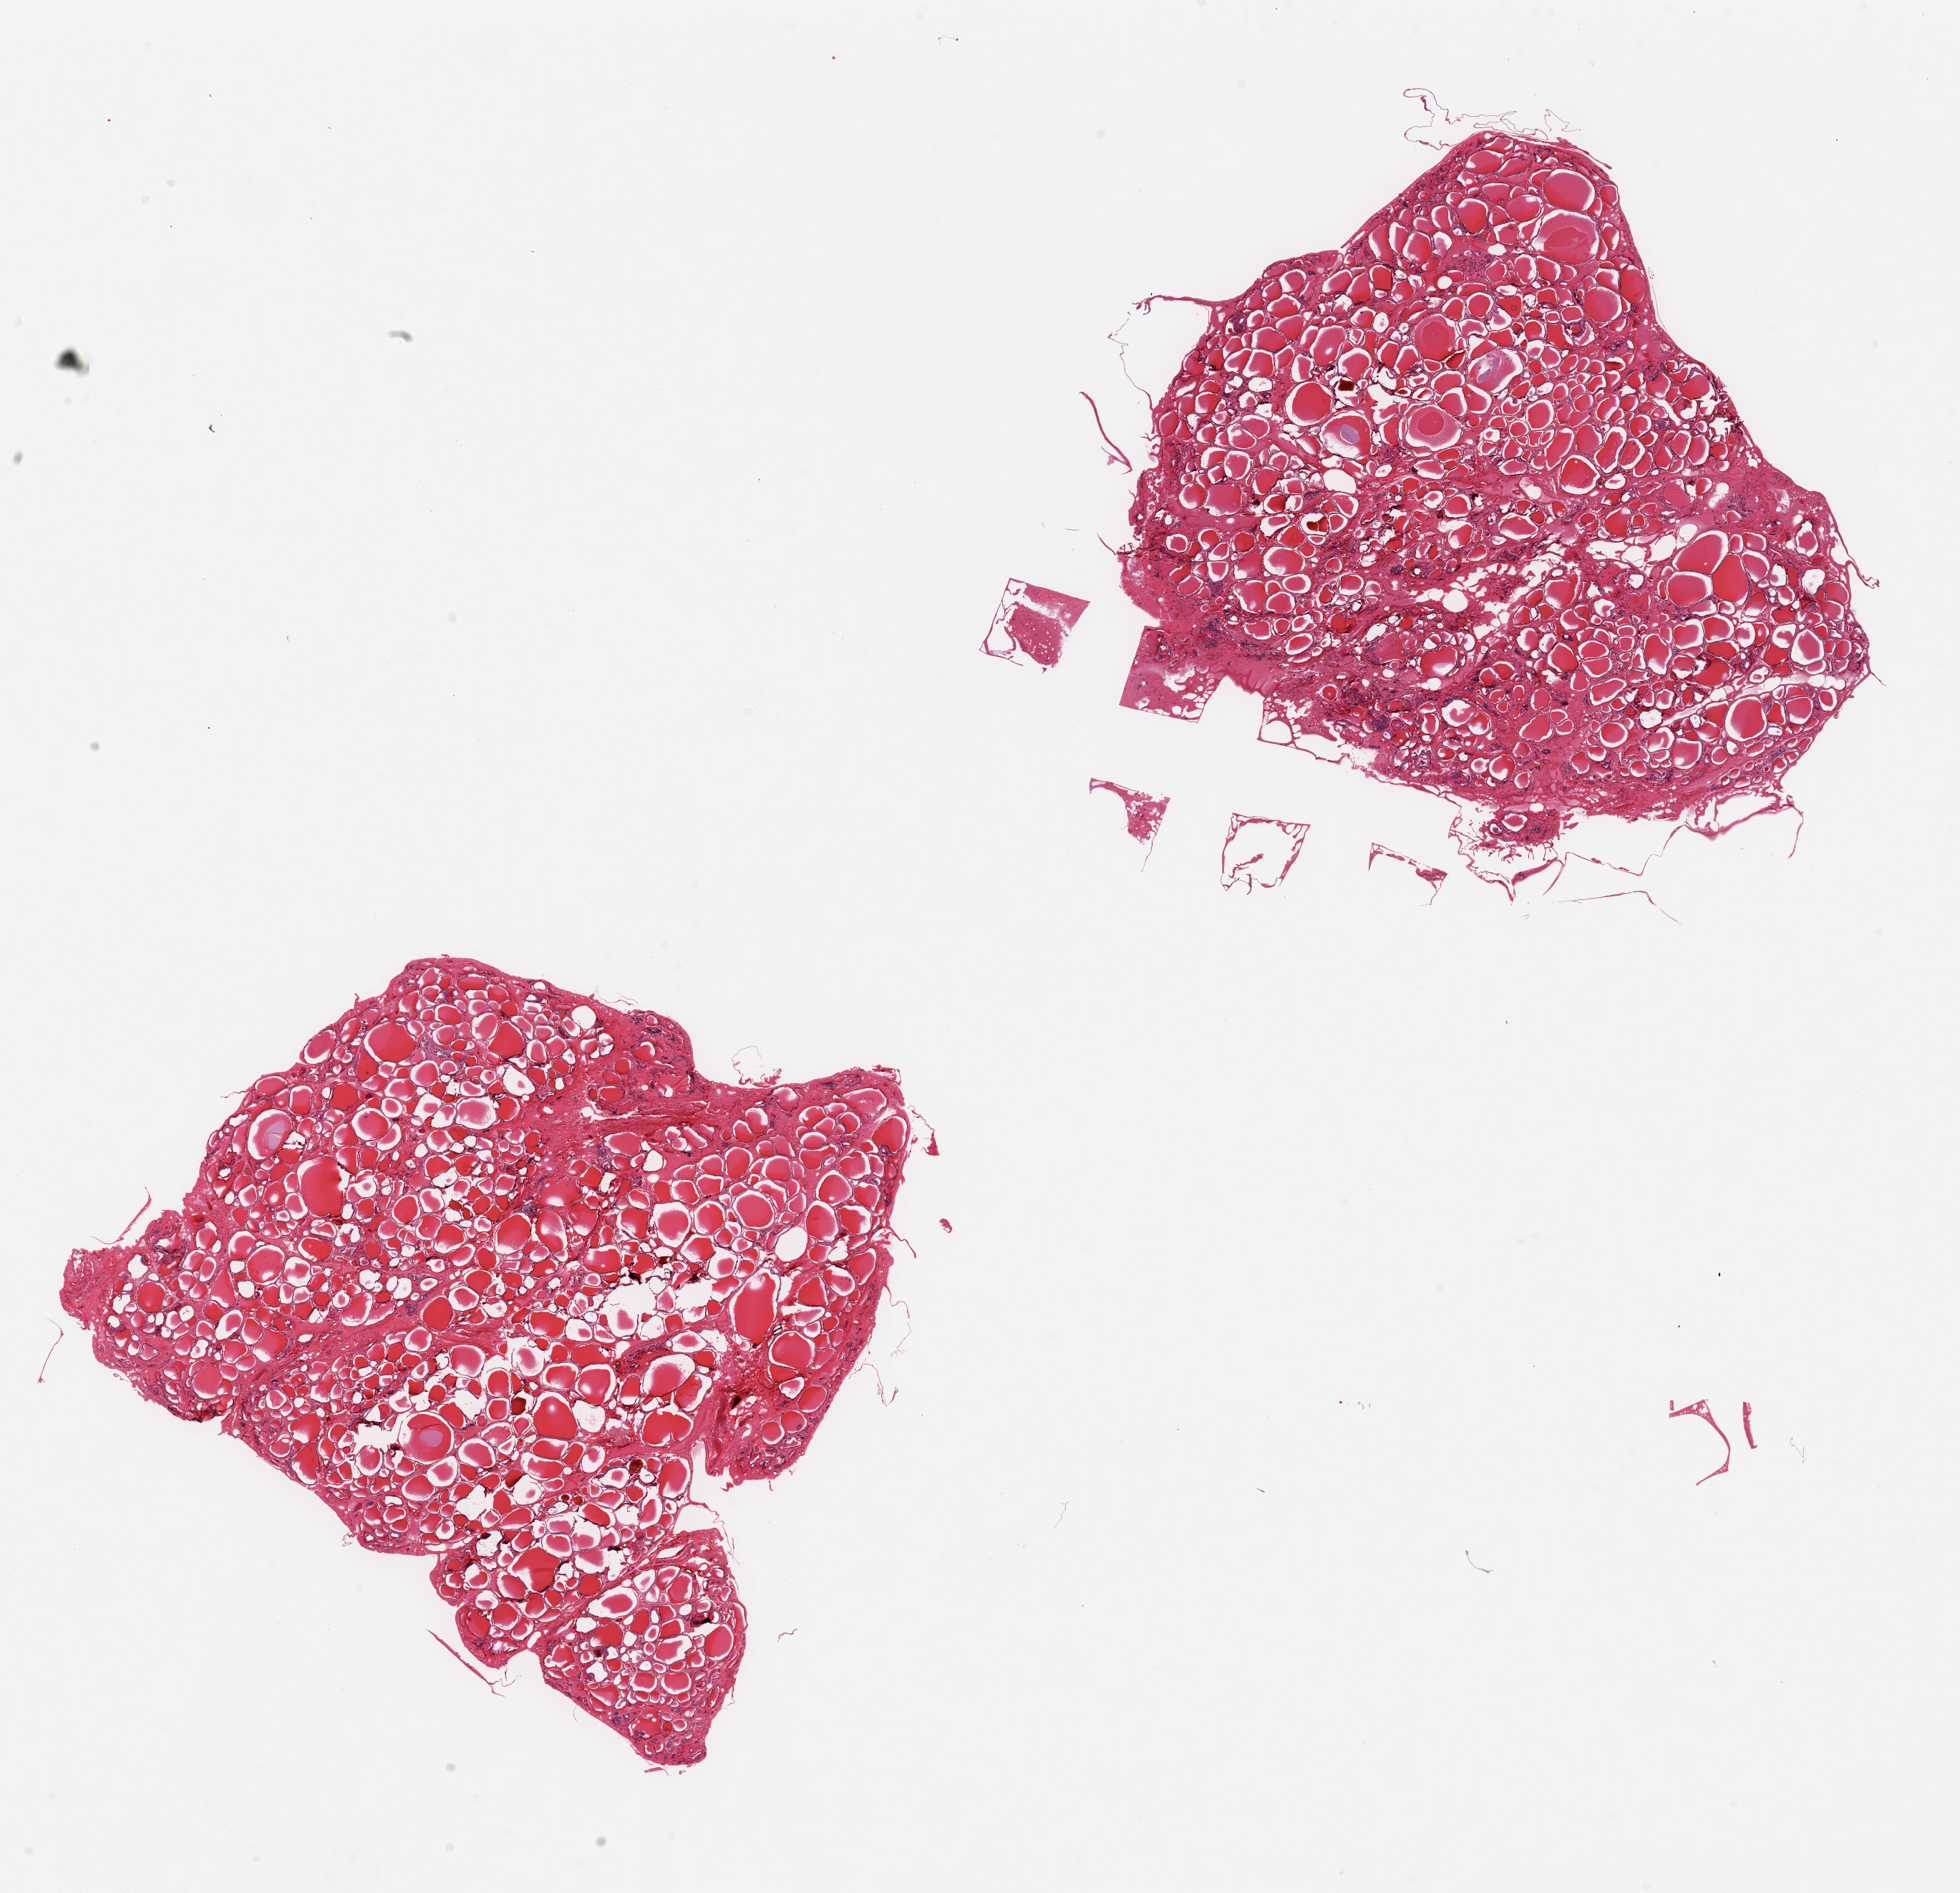
Digitized hematoxylin and eosin (H&E)-stained section, brightfield — shown as a low-resolution overview of the whole scanned area (about 21.7 x 20.9 mm); PAXgene-fixed paraffin-embedded (PFPE) section; section of thyroid (target tissue); donor tissue sample. Male donor.
Review note (as recorded): 2 pieces, no abnormalities.